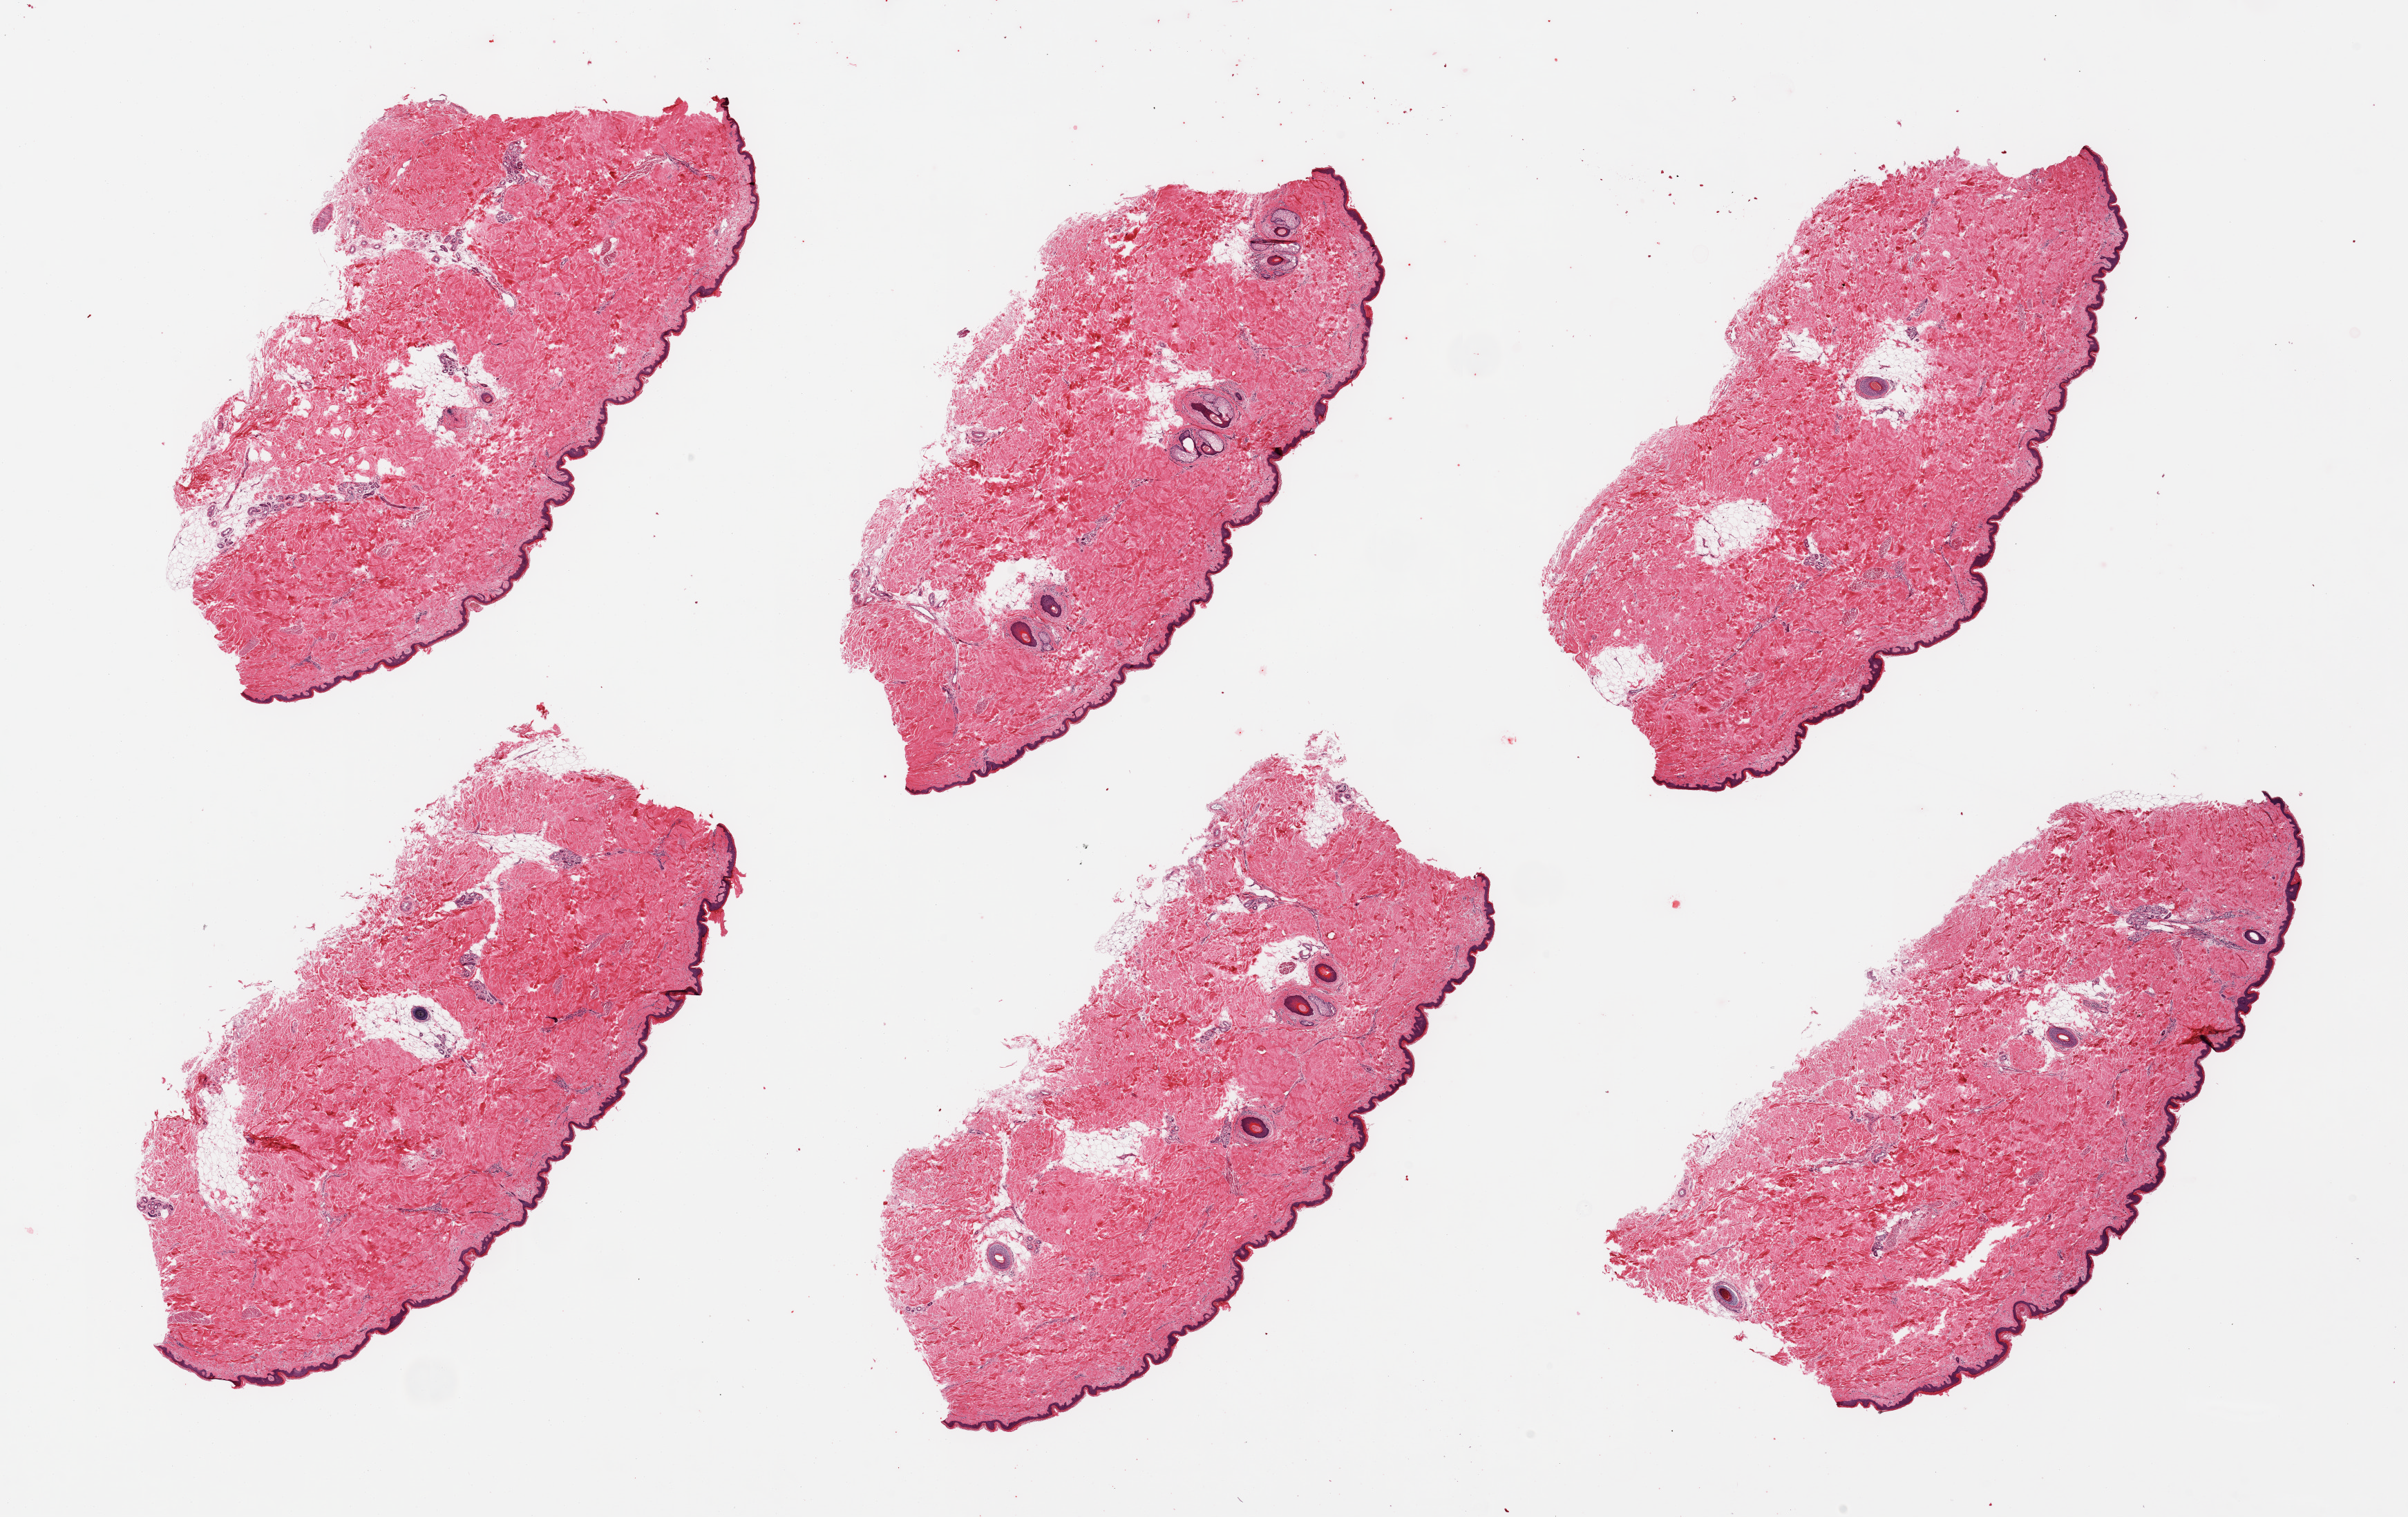
H&E whole-slide image, brightfield, shown as a low-resolution overview of the whole scanned area (about 27.6 x 17.4 mm, slide scanned at 20x); PAXgene-fixed, paraffin-embedded tissue; sampled site (target tissue): skin of lower leg; tissue donor sample. Donor sex: male.
Review note (as recorded): 6 pieces; well trimmed with minimal internal fat, epidermis measures 45 microns.